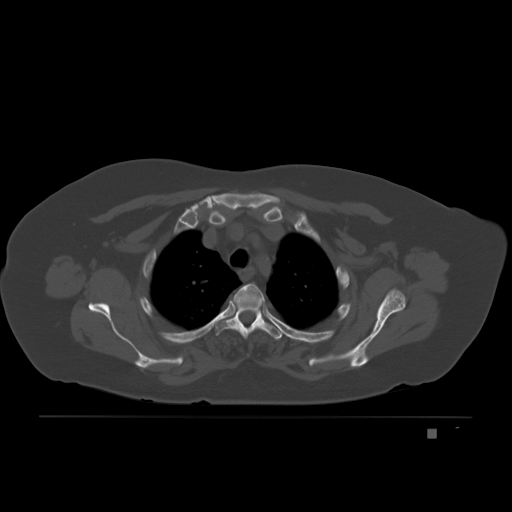
CT including the spine, one axial slice; slice 162 of 221 in the series (ordered by position); bone window (W 1800 / L 400 HU); 512 × 512 image matrix, field of view 474 × 474 mm. Female patient, age 63 years. From the clinical record (not read from this slice): primary cancer: breast.
Structures marked on this image (semi-automatic segmentation, software-assisted and operator-edited):
- T3 vertebra: bounding box [x1, y1, x2, y2] px = [213, 290, 282, 341]